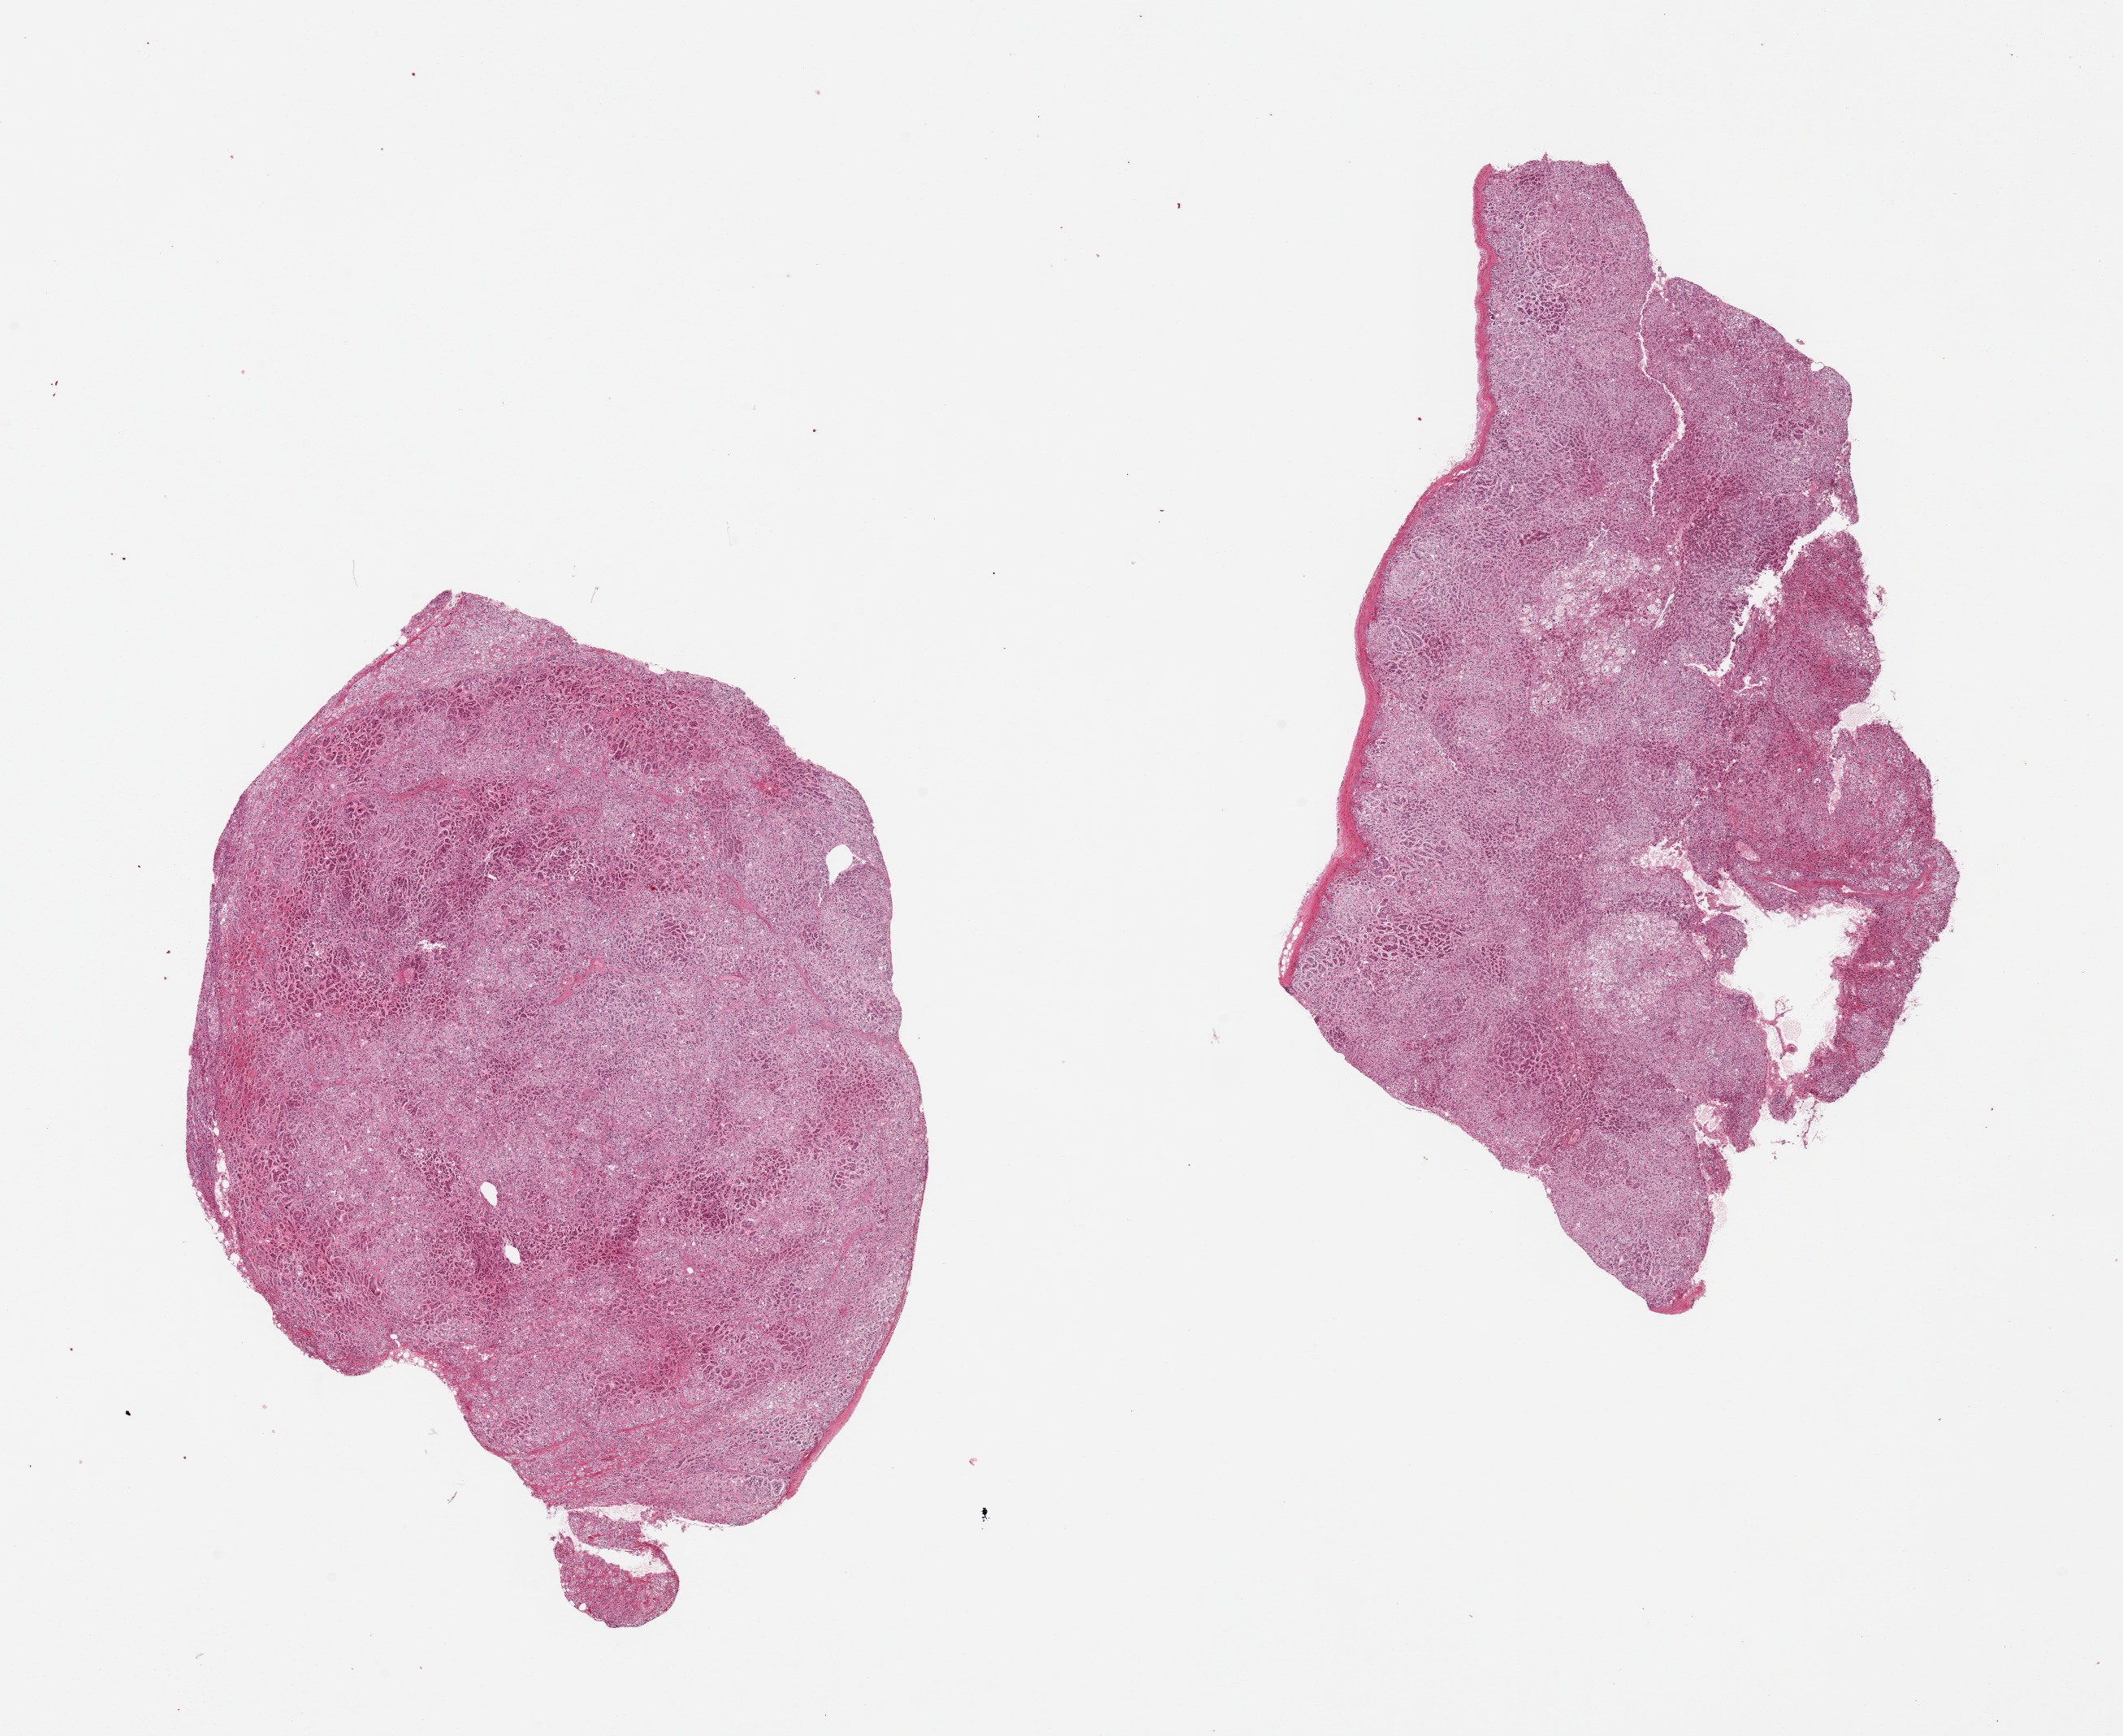
Digitized H&E-stained section, low-resolution overview of the scanned area, about 20.7 x 16.9 mm; PAXgene-fixed, paraffin-embedded tissue; target tissue: adrenal gland; tissue donor sample. Male donor.
- review note (as recorded): 2 pieces, 9x6 and 8x7.5mm, all cortex, moderately-markedly autolyzed